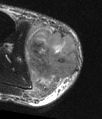
MRI of an extremity soft-tissue mass, one axial slice; slice 21 of 48 in the series (ordered by position); T2-weighted fat-saturated; MR volume resampled by the dataset authors to the PET/CT grid (not the native acquisition matrix); 3.27 mm slice thickness; 102 × 119 image matrix, field of view 100 × 116 mm. Male patient. From the clinical record (not read from this slice): histological type: pleiomorphic liposarcoma; grade: high; site of the primary tumour: right calf.
Annotated regions visible in this slice (expert contour drawn on MRI and transferred to this co-registered scan by the dataset authors):
- gross tumour volume including surrounding oedema: bounding box (x1, y1, x2, y2) in pixels: (26, 24, 79, 100)
- gross tumour volume (mass): (26, 28, 79, 84)